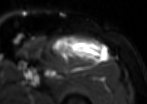
MRI of an extremity soft-tissue mass, one axial slice. T2-weighted fat-saturated. MR volume resampled by the dataset authors to the PET/CT grid (not the native acquisition matrix). 3.27 mm slice thickness. 147 × 104 image matrix, field of view 144 × 102 mm. Male patient. Case-level facts recorded for this patient, not image findings: histological type: extraskeletal osteosarcoma; grade: high; site of the primary tumour: thigh.
Annotated regions visible in this slice (expert contour drawn on MRI and transferred to this co-registered scan by the dataset authors):
- gross tumour volume (mass): box from (x=53, y=35) to (x=107, y=63) px